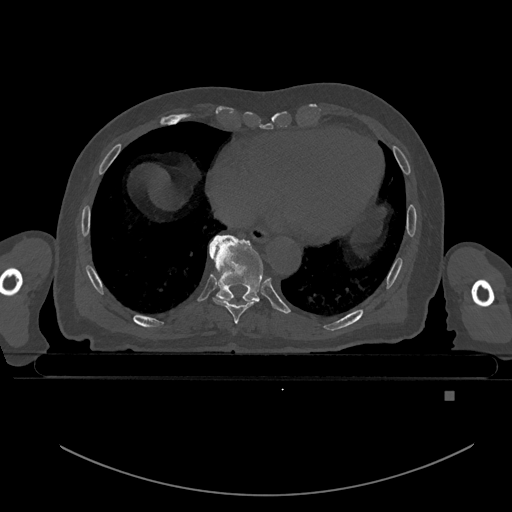
CT including the spine, one axial slice; position 174 of 969 along the scan axis; bone window (W 1800 / L 400 HU); 0.5 mm slice thickness; 512 × 512 image matrix, field of view 456 × 456 mm. Male patient, age 82 years. Case-level facts recorded for this patient, not image findings: primary cancer: prostate; vertebrae with lytic lesions (as recorded): T11, T9, T8, T2.
Outlined on this slice (semi-automatically segmented with operator editing):
- T8 vertebra: box from (x=212, y=297) to (x=255, y=324) px
- T9 vertebra: (x=209, y=235)–(x=264, y=303)